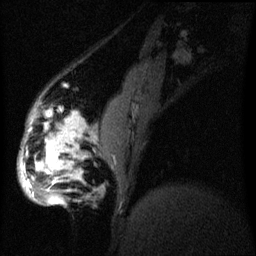
Breast MRI (dynamic contrast-enhanced), one sagittal slice. Dynamic contrast-enhanced series, image 2 of 3 at this slice position (ordered by acquisition). 1.5 T. TE 4.2 ms, TR 8 ms. 2.2 mm slice thickness. 256 × 256 image matrix, field of view 200 × 200 mm. Patient: female, 50 years.
Outlined on this slice (semi-automatic segmentation, software-assisted and operator-edited):
- analysis volume of interest (the breast-tissue region the enhancement analysis was run in; not a lesion): bounding box <19,112,73,207> (left, top, right, bottom; pixels)
- tumour enhancement mask (voxels above the 70 % enhancement threshold inside the analysis volume of interest): <22,120,72,203>